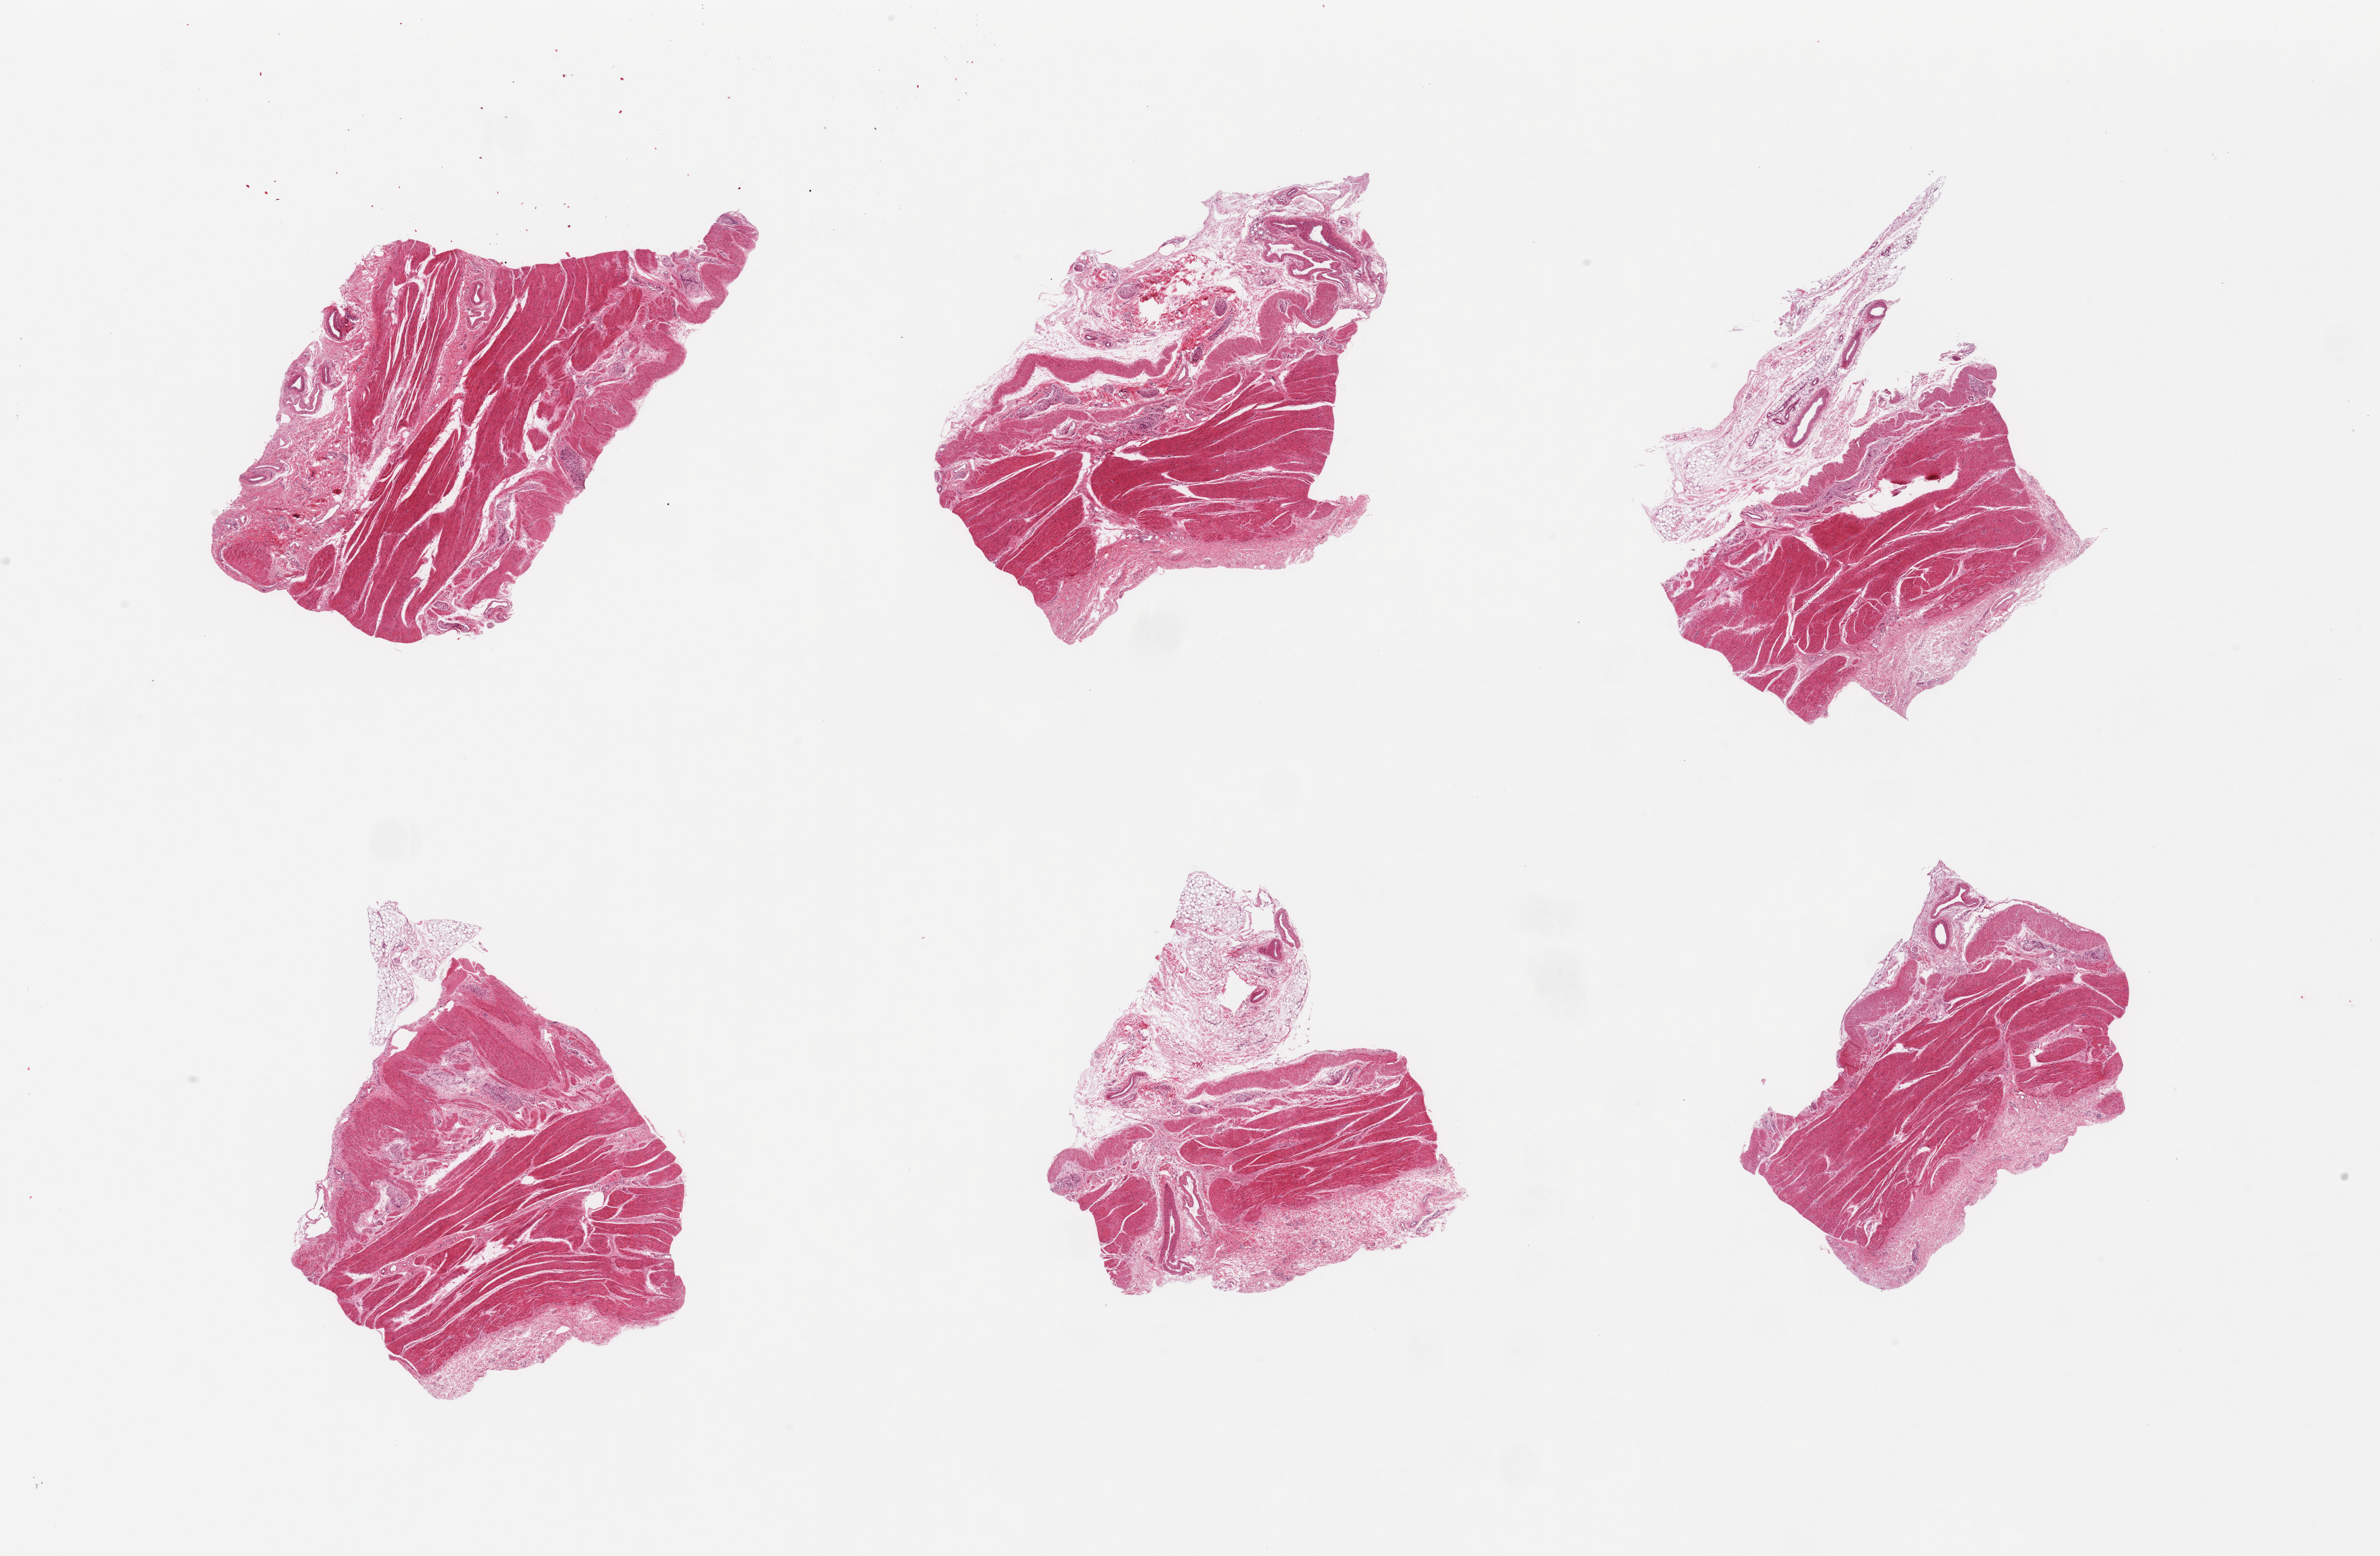
Haematoxylin and eosin whole-slide image — a low-resolution overview of the entire scanned area, about 28.5 x 18.7 mm; PAXgene-fixed paraffin-embedded (PFPE) section; section of transverse colon (target tissue); tissue donor sample. Donor: male.
- reviewer comment on this tissue sample: 2 pieces; muscularis and submucosa, no mucosa [could be used to compare to sigmoid colon]